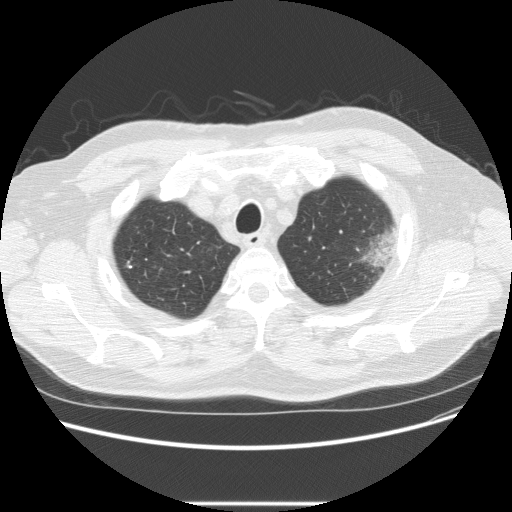
Axial slice from a low-dose chest CT screening exam; baseline annual screen; lung window (W 1500 / L -600 HU); 120 kVp. Male participant, aged 73 years at enrolment. Former smoker at enrolment.
- Expert reader's lesion annotation, bounding box (x1, y1, x2, y2) in pixels: (332, 216, 406, 282).
- The screening reader recorded 2 non-calcified nodules or masses ≥4 mm on this exam (left upper lobe, right upper lobe); which of them this box marks is not recorded.